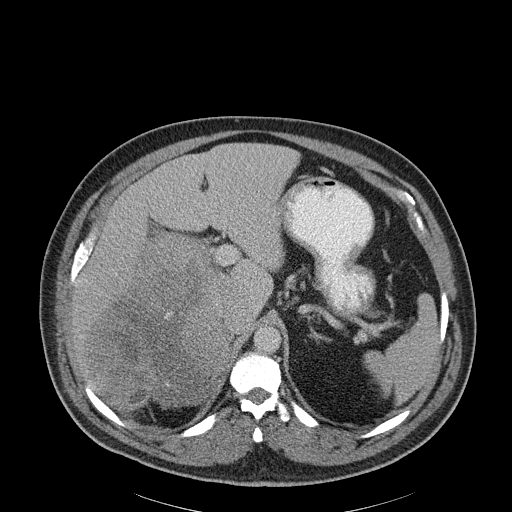
Contrast-enhanced abdominal CT, one axial slice; soft-tissue window (W 400 / L 40 HU); 512 × 512 image matrix, field of view 464 × 464 mm. Patient: male, 56 years. Case-level facts recorded for this patient, not image findings: diagnosis: adrenocortical carcinoma; tumour side: right adrenal.
Annotated regions visible in this slice (semi-automatically segmented with operator editing):
- mass: bounding box (x1, y1, x2, y2) in pixels: (89, 235, 222, 408)